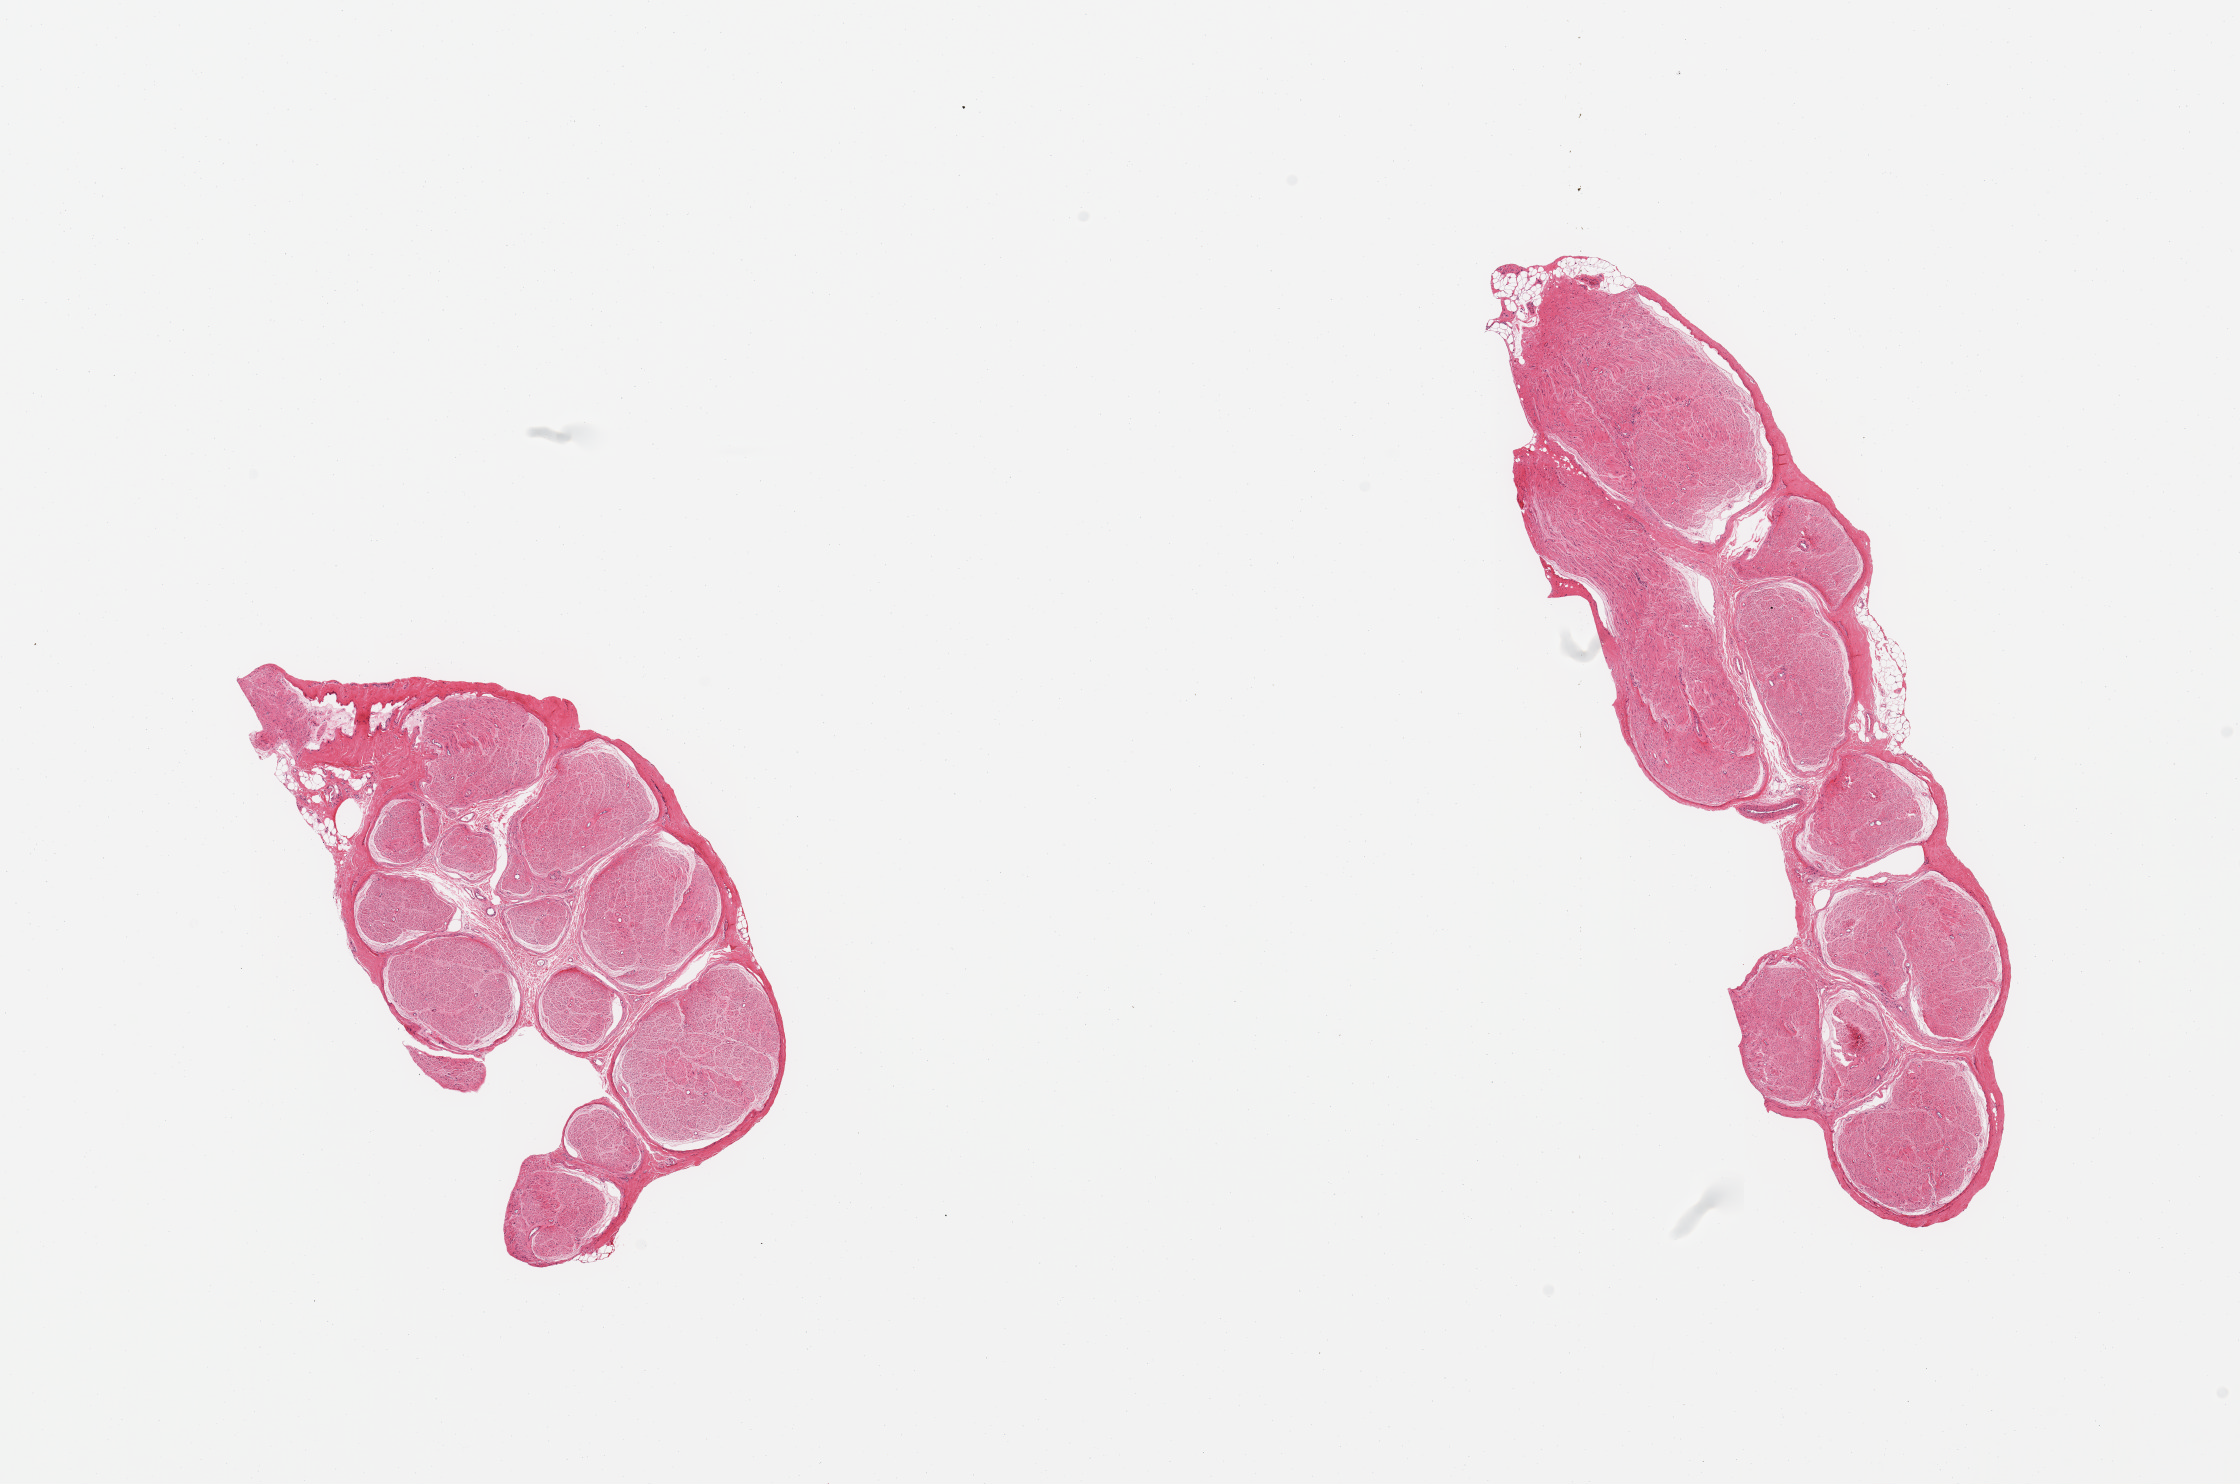
H&E whole-slide image — low-resolution overview of the scanned area, about 17.7 x 11.7 mm. PAXgene-fixed, paraffin-embedded tissue. Section of tibial nerve (target tissue). Tissue donor sample.
- reviewer comment on this tissue sample: 2 pieces; relatively well trimmed with minimal attached fat